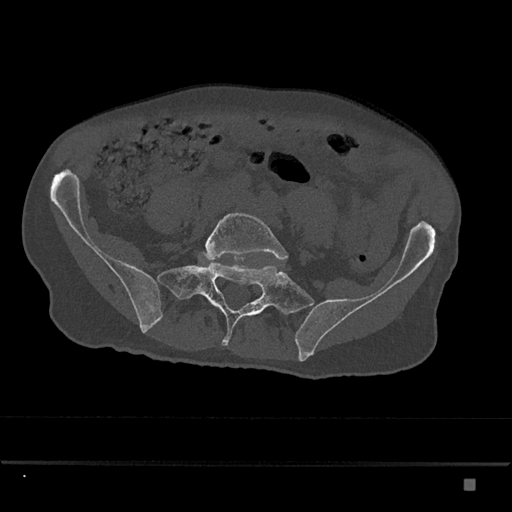
CT including the spine, one axial slice. Position 243 of 797 along the scan axis. Reconstruction kernel Br40s/3. Bone window (W 1800 / L 400 HU). 512 × 512 image matrix. Male patient, age 72 years. From the clinical record (not read from this slice): primary cancer: prostate.
Outlined on this slice (semi-automatic segmentation, software-assisted and operator-edited):
- L5 vertebra: bounding box (x1, y1, x2, y2) in pixels: (204, 213, 288, 261)